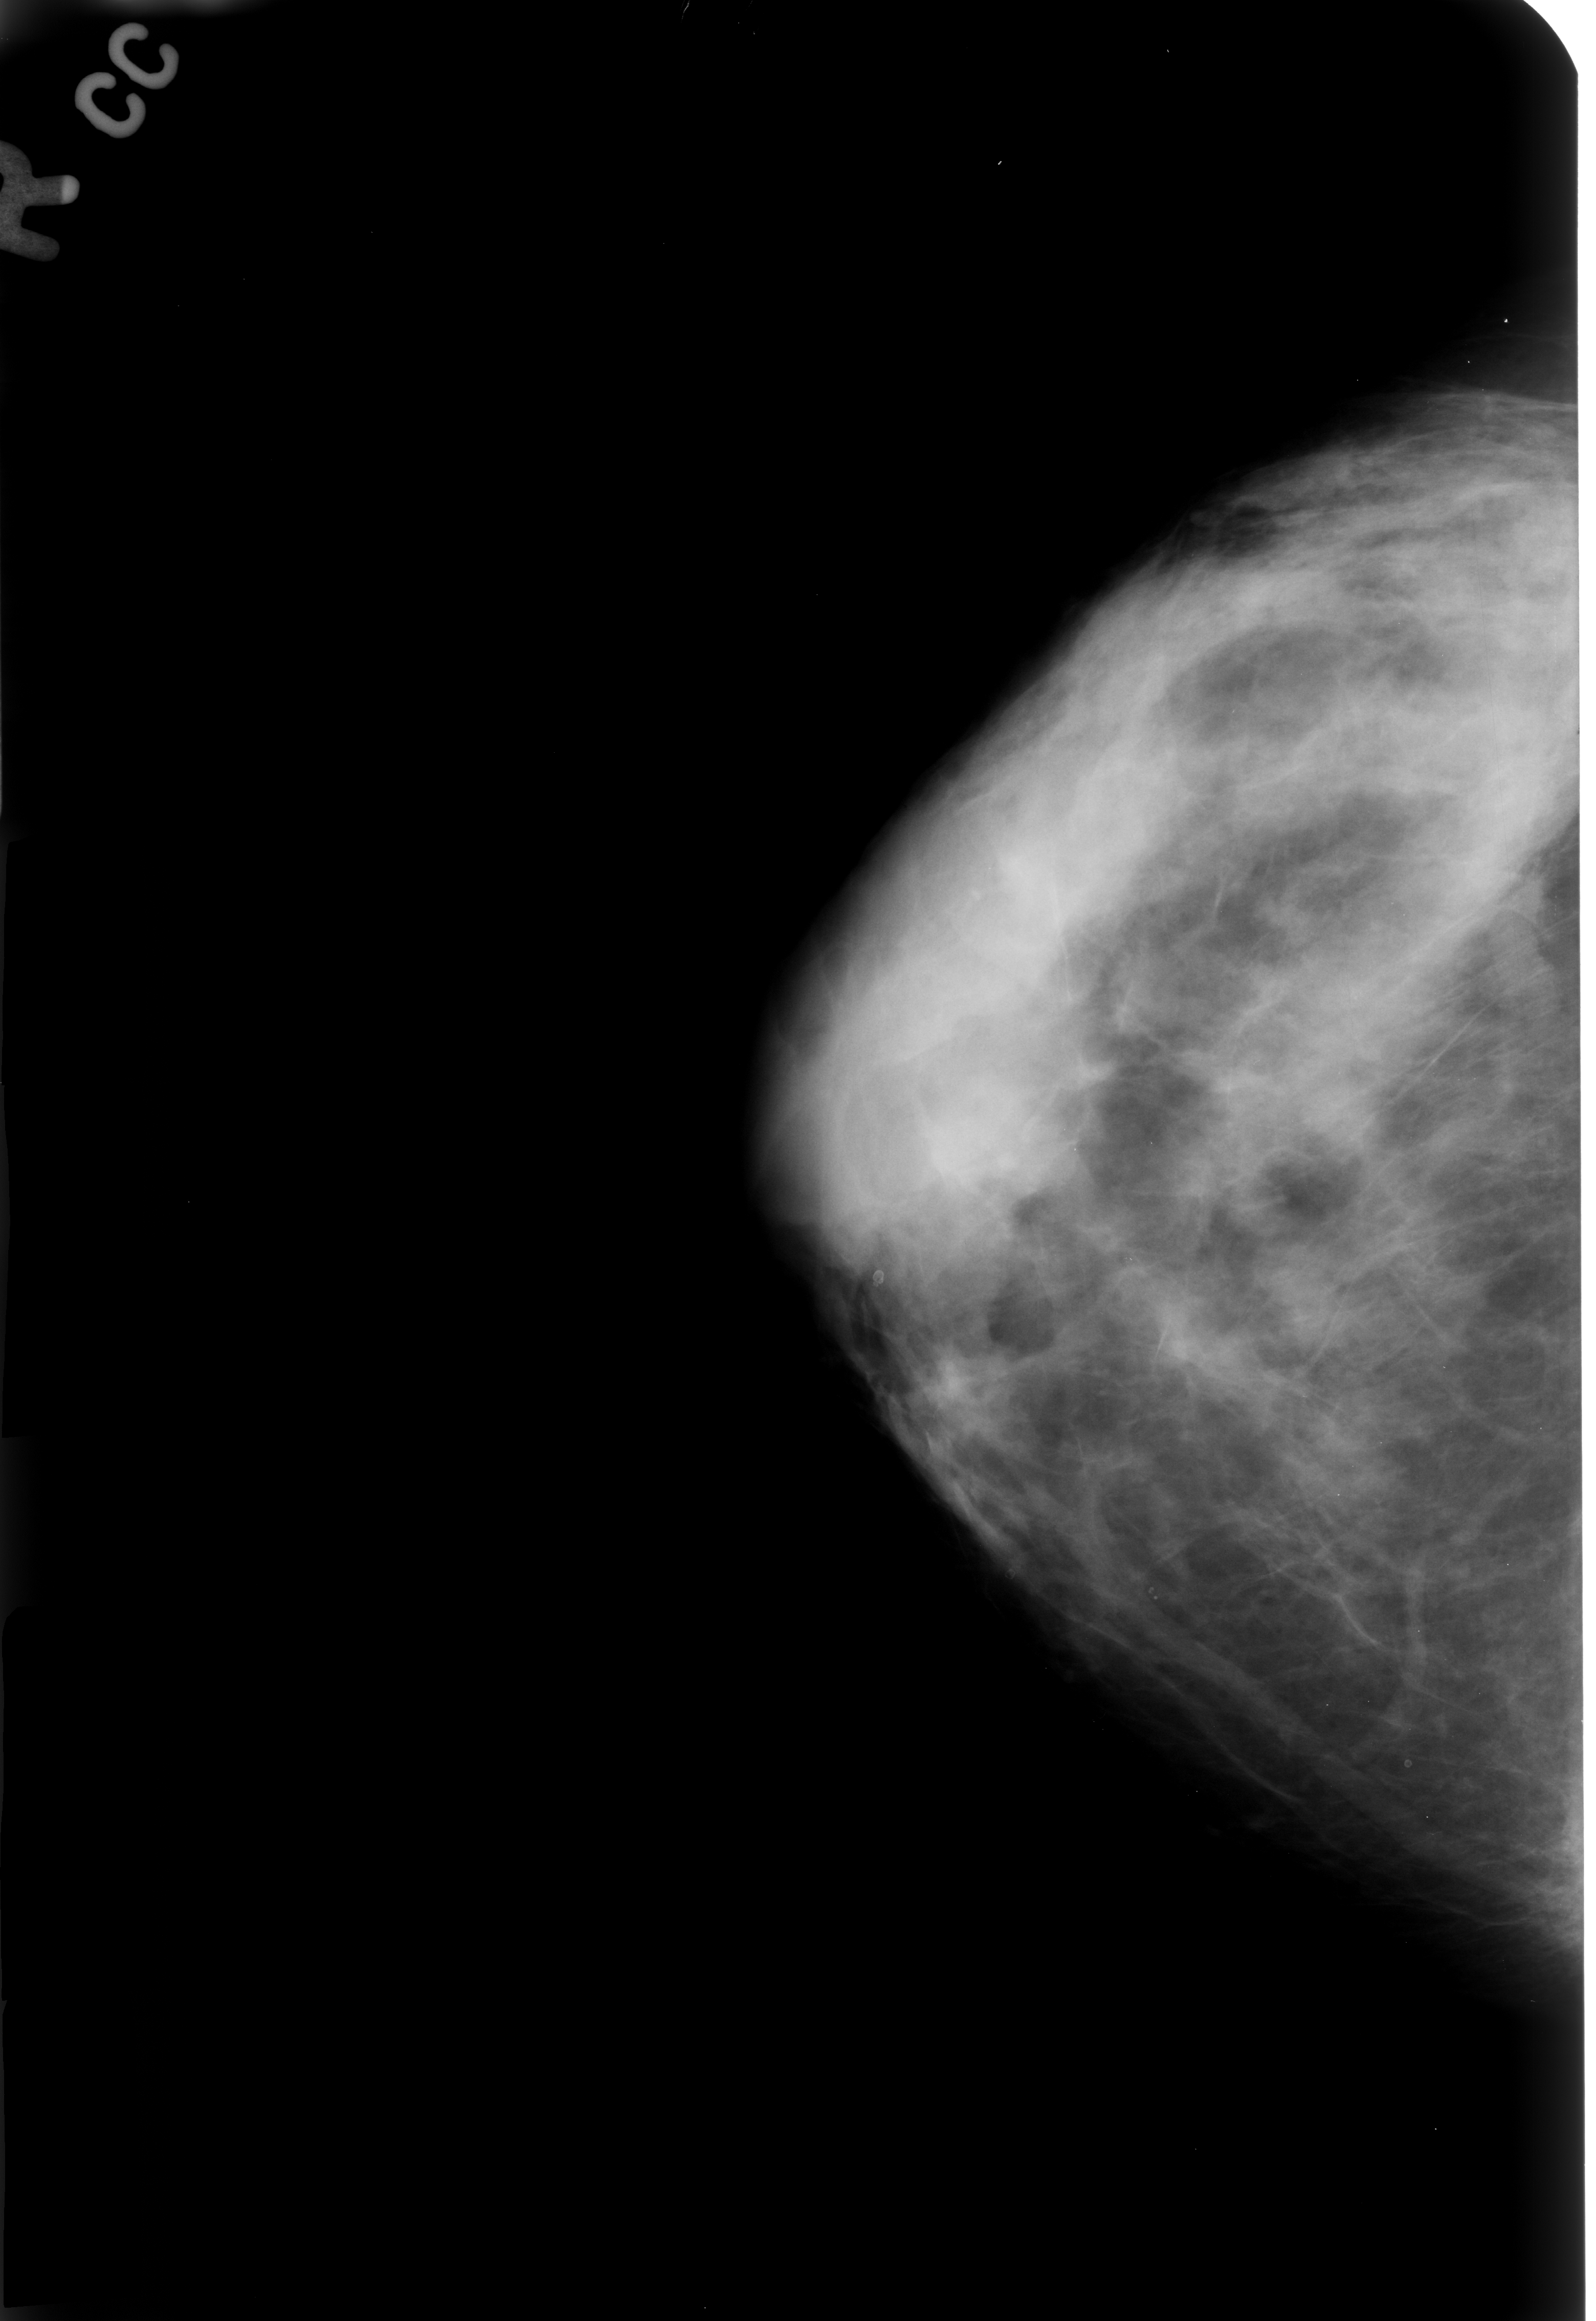
Mammogram (digitized film); right breast; CC view; breast composition: heterogeneously dense (BI-RADS density category 3 of 4).
Marked abnormality: calcifications, morphology lucent center; BI-RADS assessment category 2; subtlety rating 3 on a 1 (subtle) to 5 (obvious) scale; benign; no additional work-up was recommended (benign without callback).